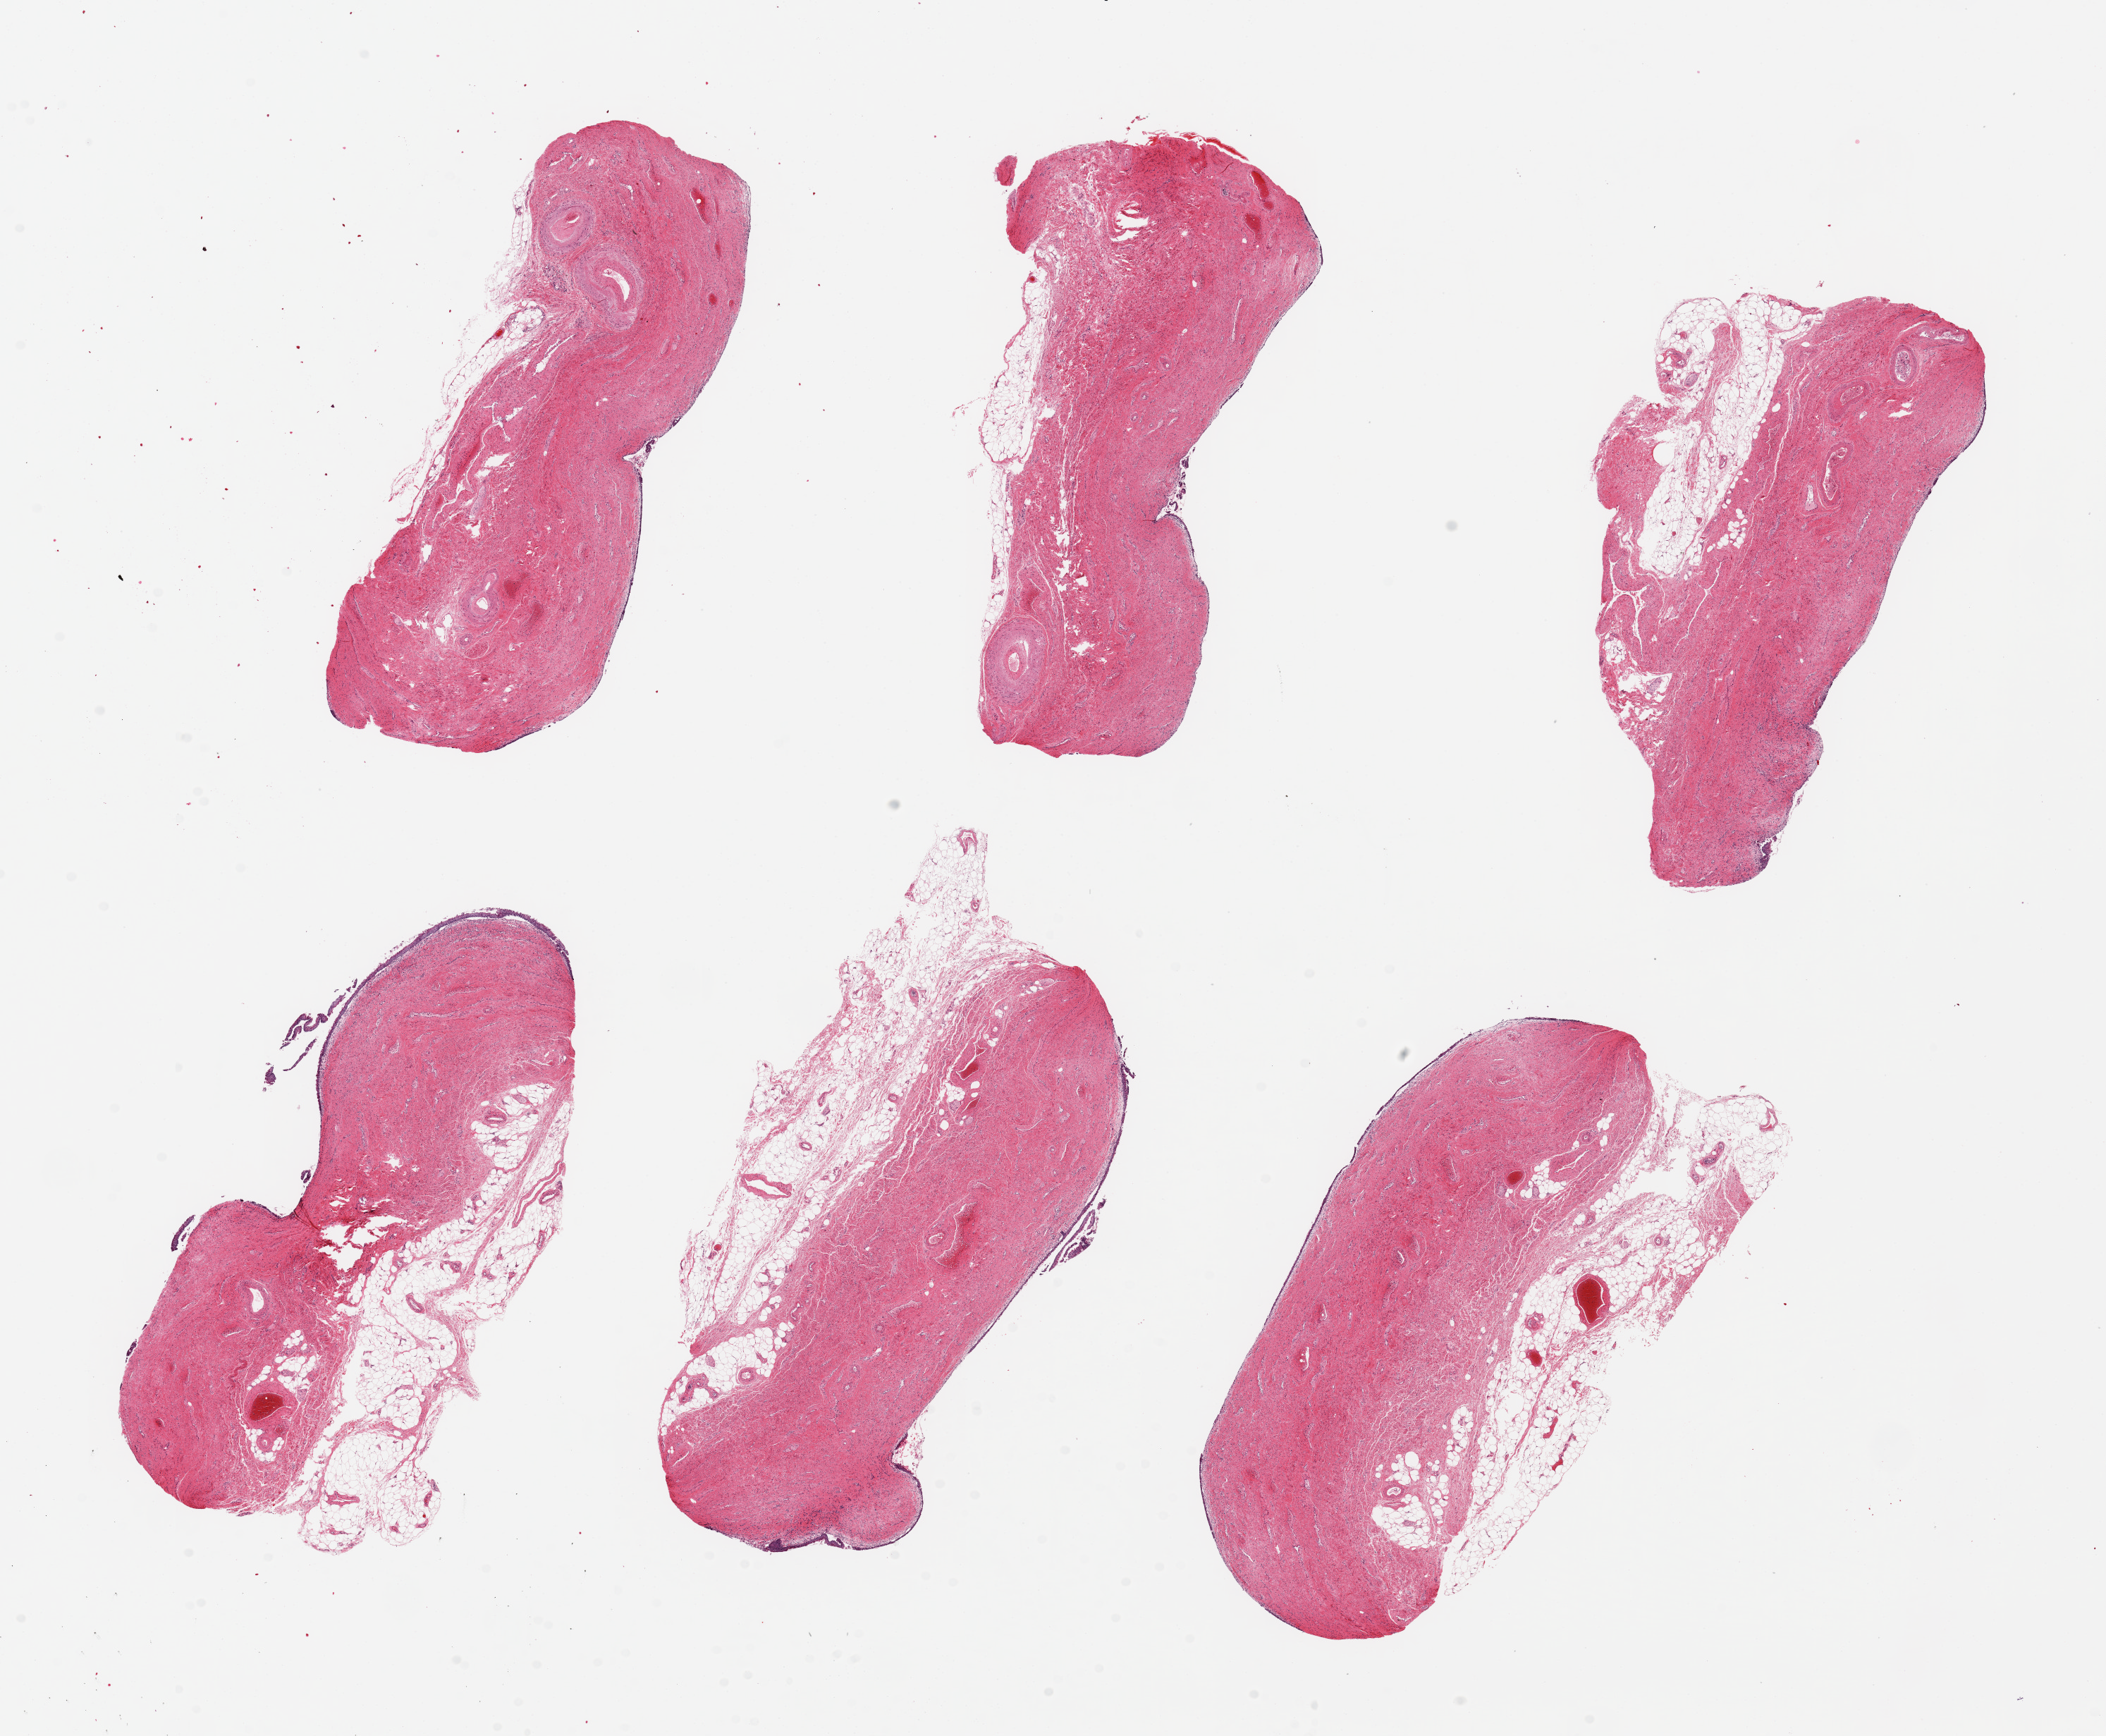
H&E whole-slide image — low-resolution overview of the scanned area, about 23.6 x 19.5 mm; PAXgene-fixed paraffin-embedded (PFPE) section; sampled site (target tissue): vagina; tissue donor sample.
* pathologist's review note for this sample: 6 pieces, up to 8x4mm; atrophic partially sloughed epithelium